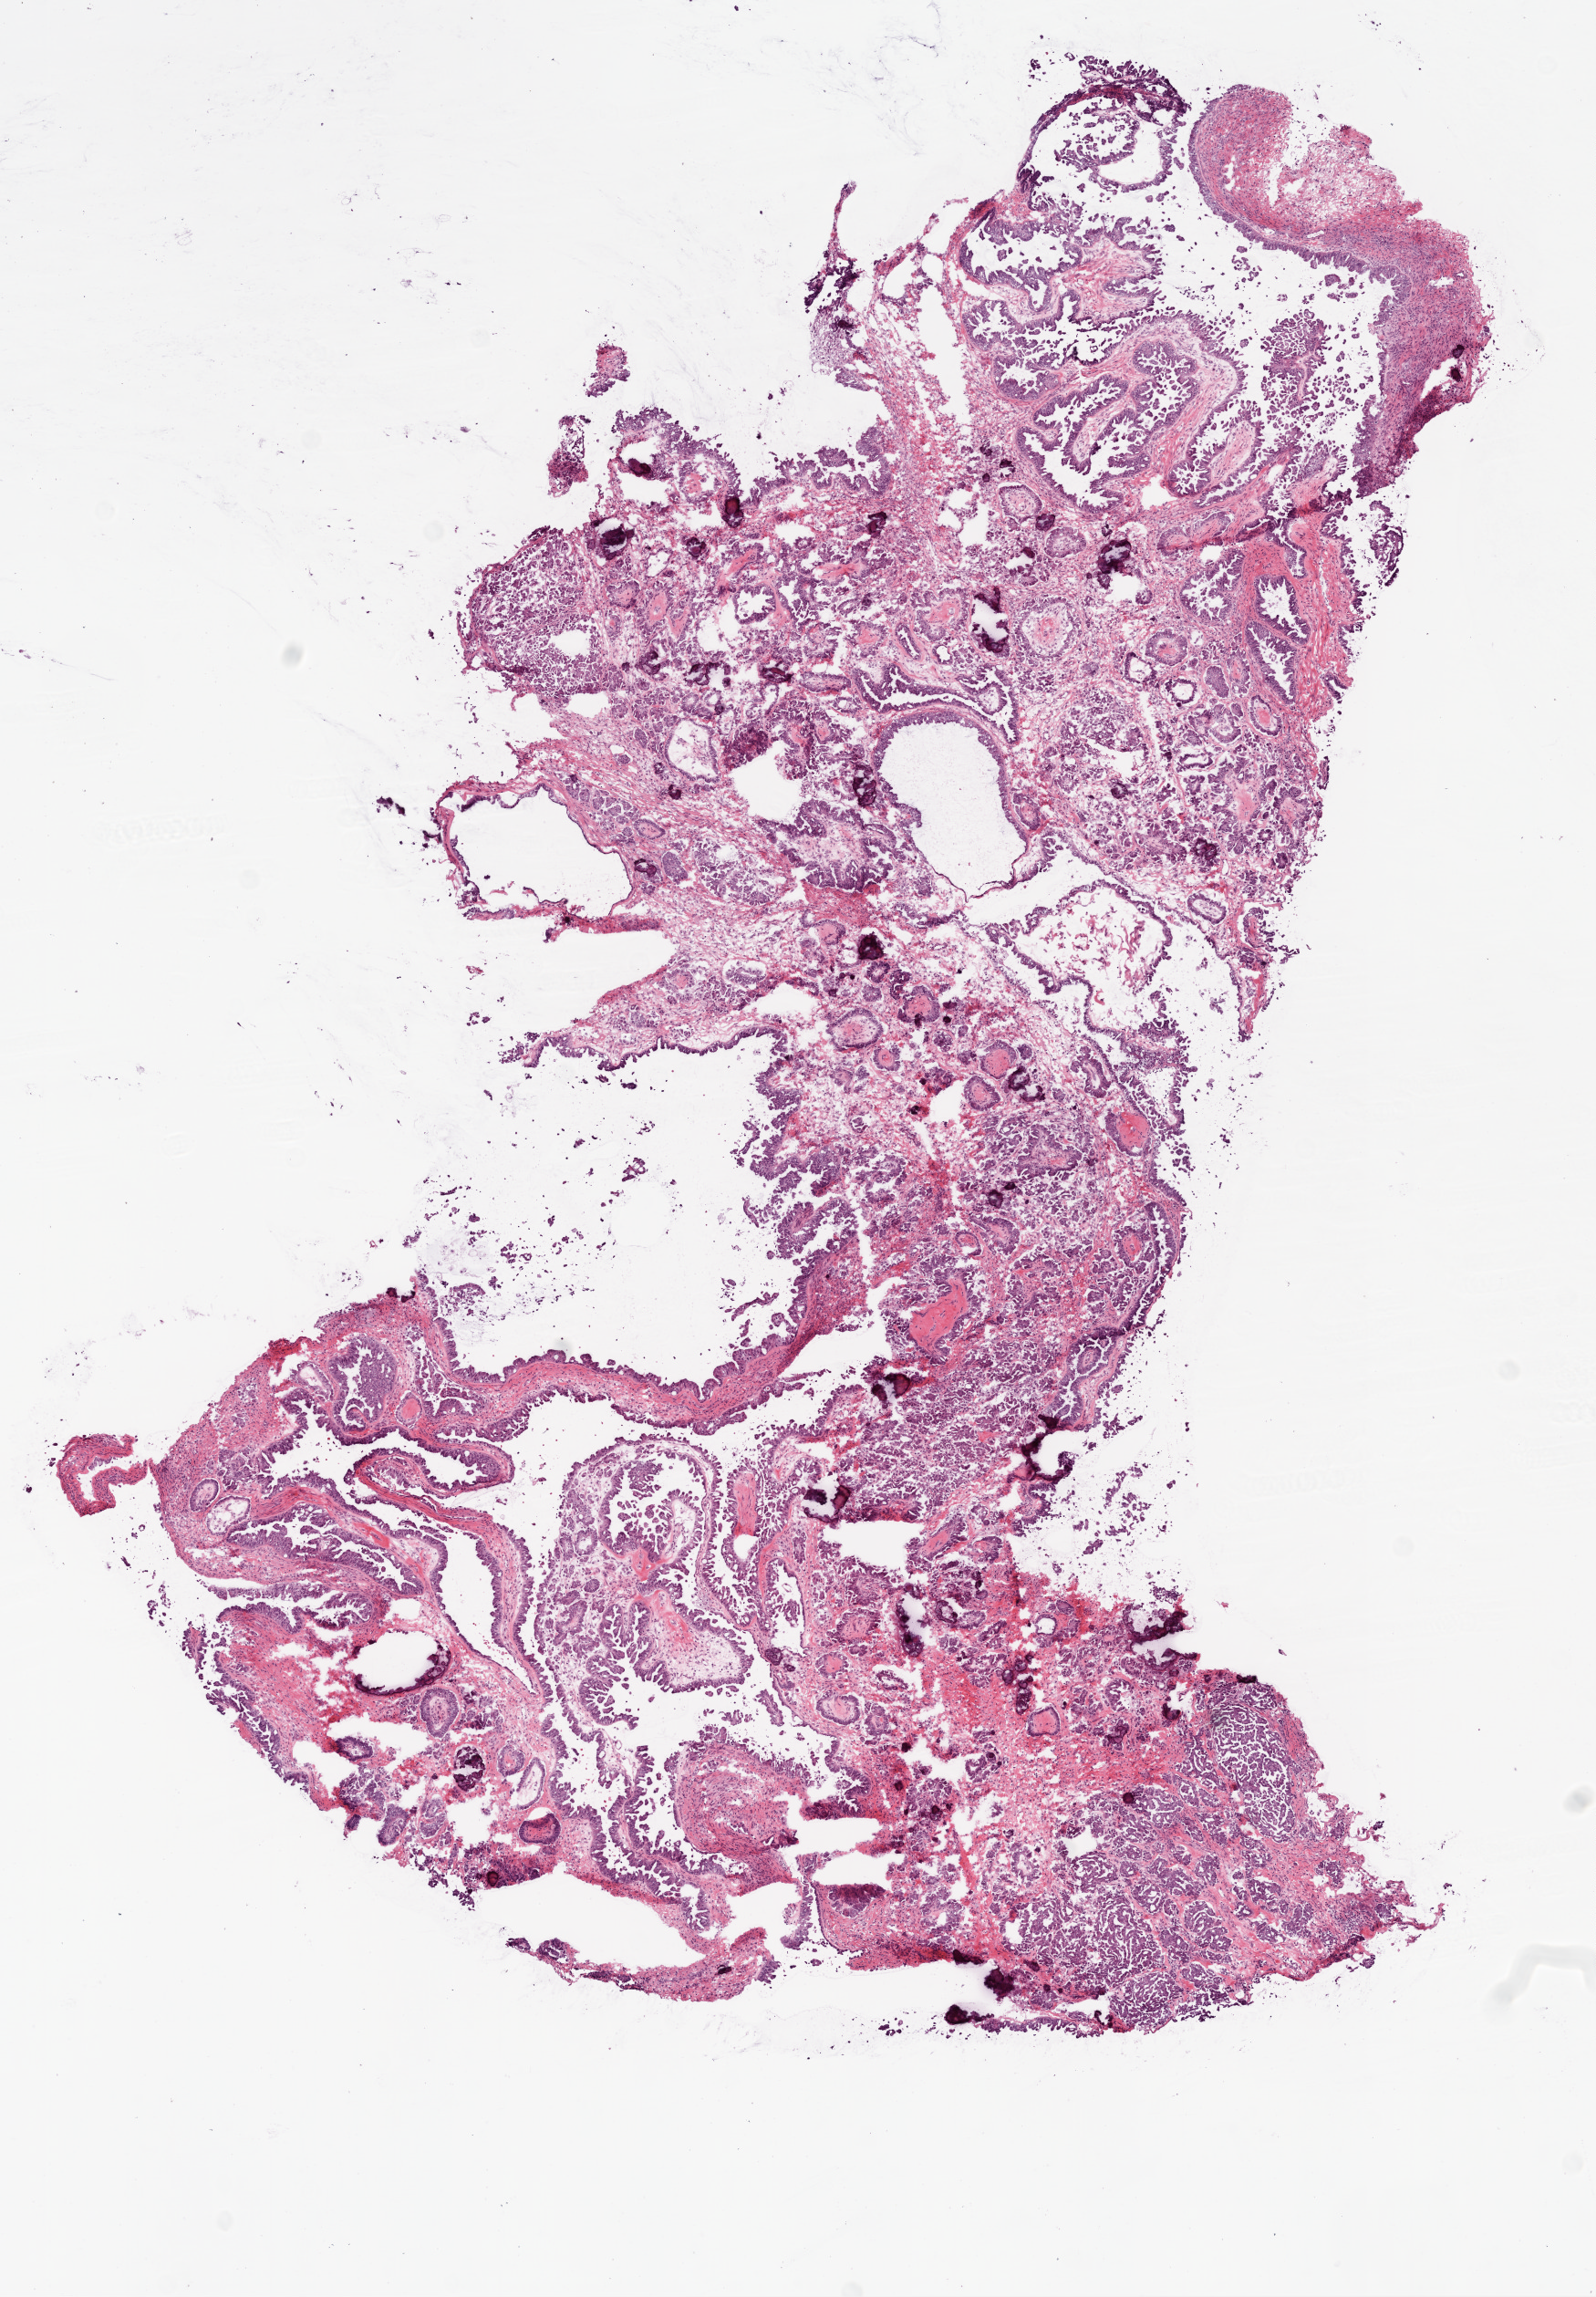
H&E whole-slide image — whole scanned area (about 7.0 x 10.1 mm, slide scanned at 20x) shown as a low-resolution overview. Frozen section from the bottom of the tissue portion. Sample: primary tumour, ovary. Female, age 78 years at initial diagnosis. Histologic grade: G1 (well differentiated). Slide review estimates, as recorded: tumour cells 50%, tumour nuclei 70%, normal cells 0%, stromal cells 50%, necrosis 0%.
- pathologic diagnosis: Serous cystadenocarcinoma, NOS
- FIGO stage: IIIC